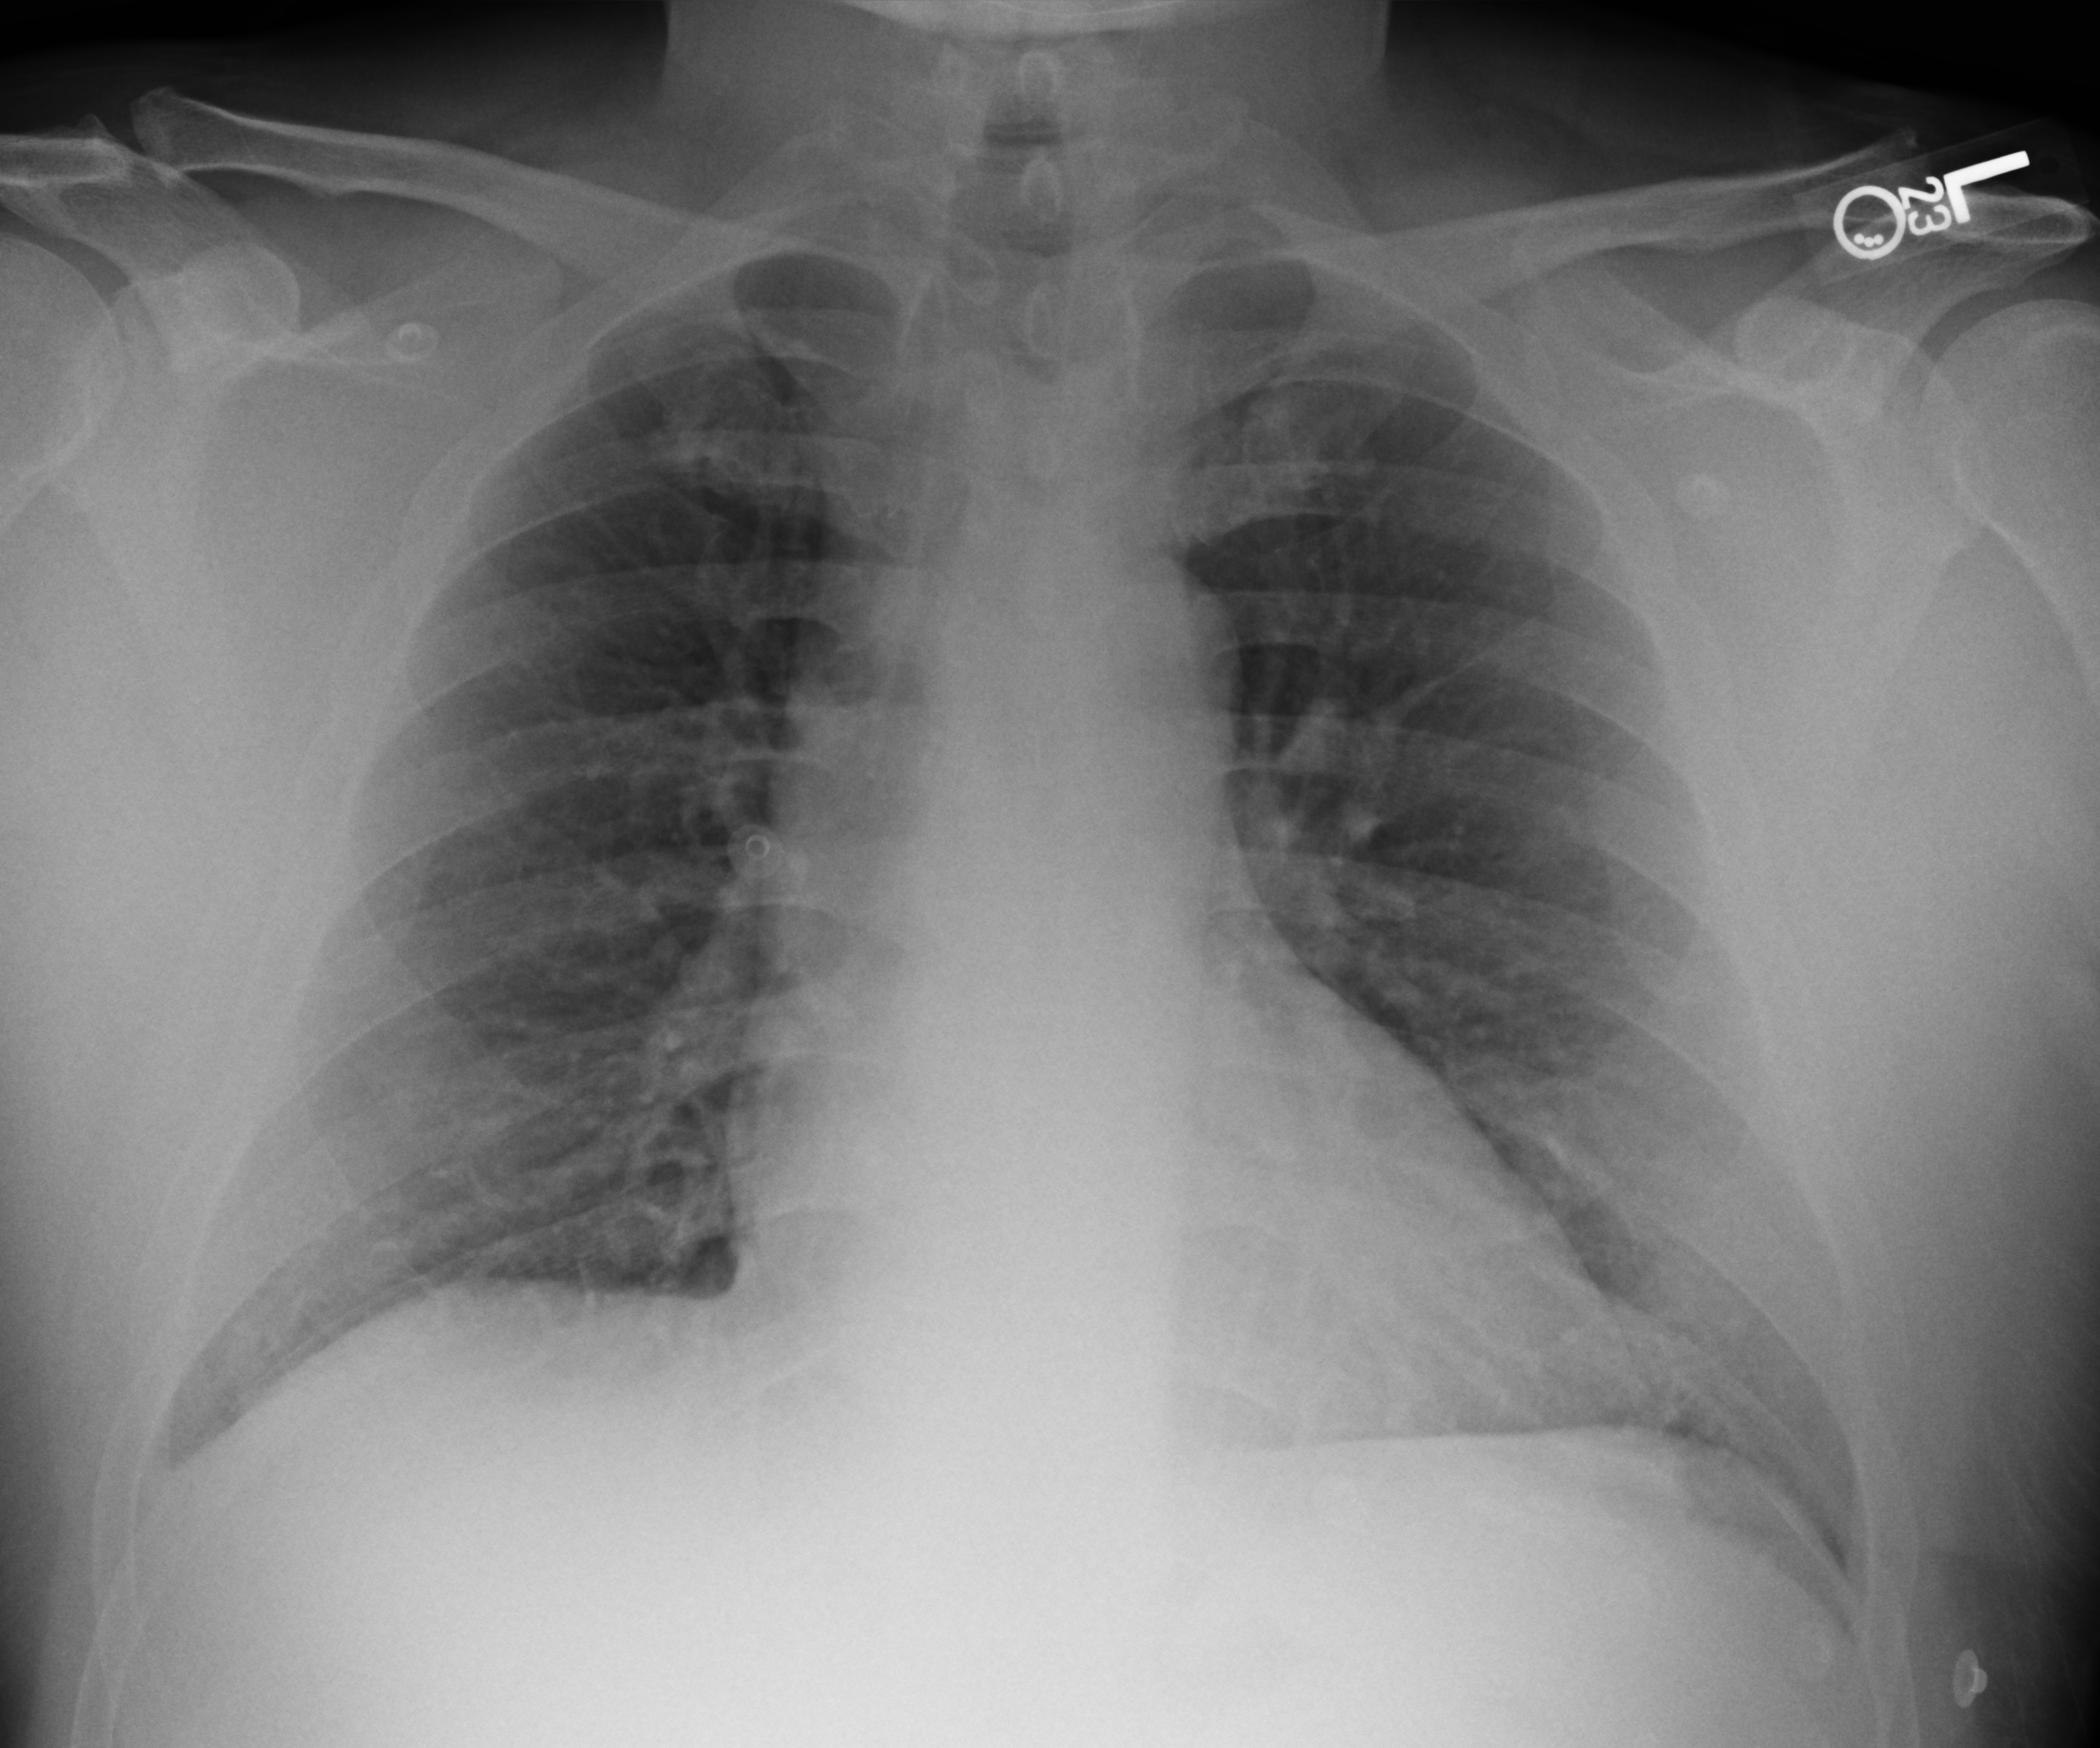
Portable chest radiograph; anteroposterior (AP) projection. Male patient hospitalised with COVID-19, age 18–59 years.
Hospital-stay facts (about this admission, not read from this image; timing relative to this image not recorded): mechanically ventilated during this hospital stay: no; admitted to intensive care during this hospital stay: no.